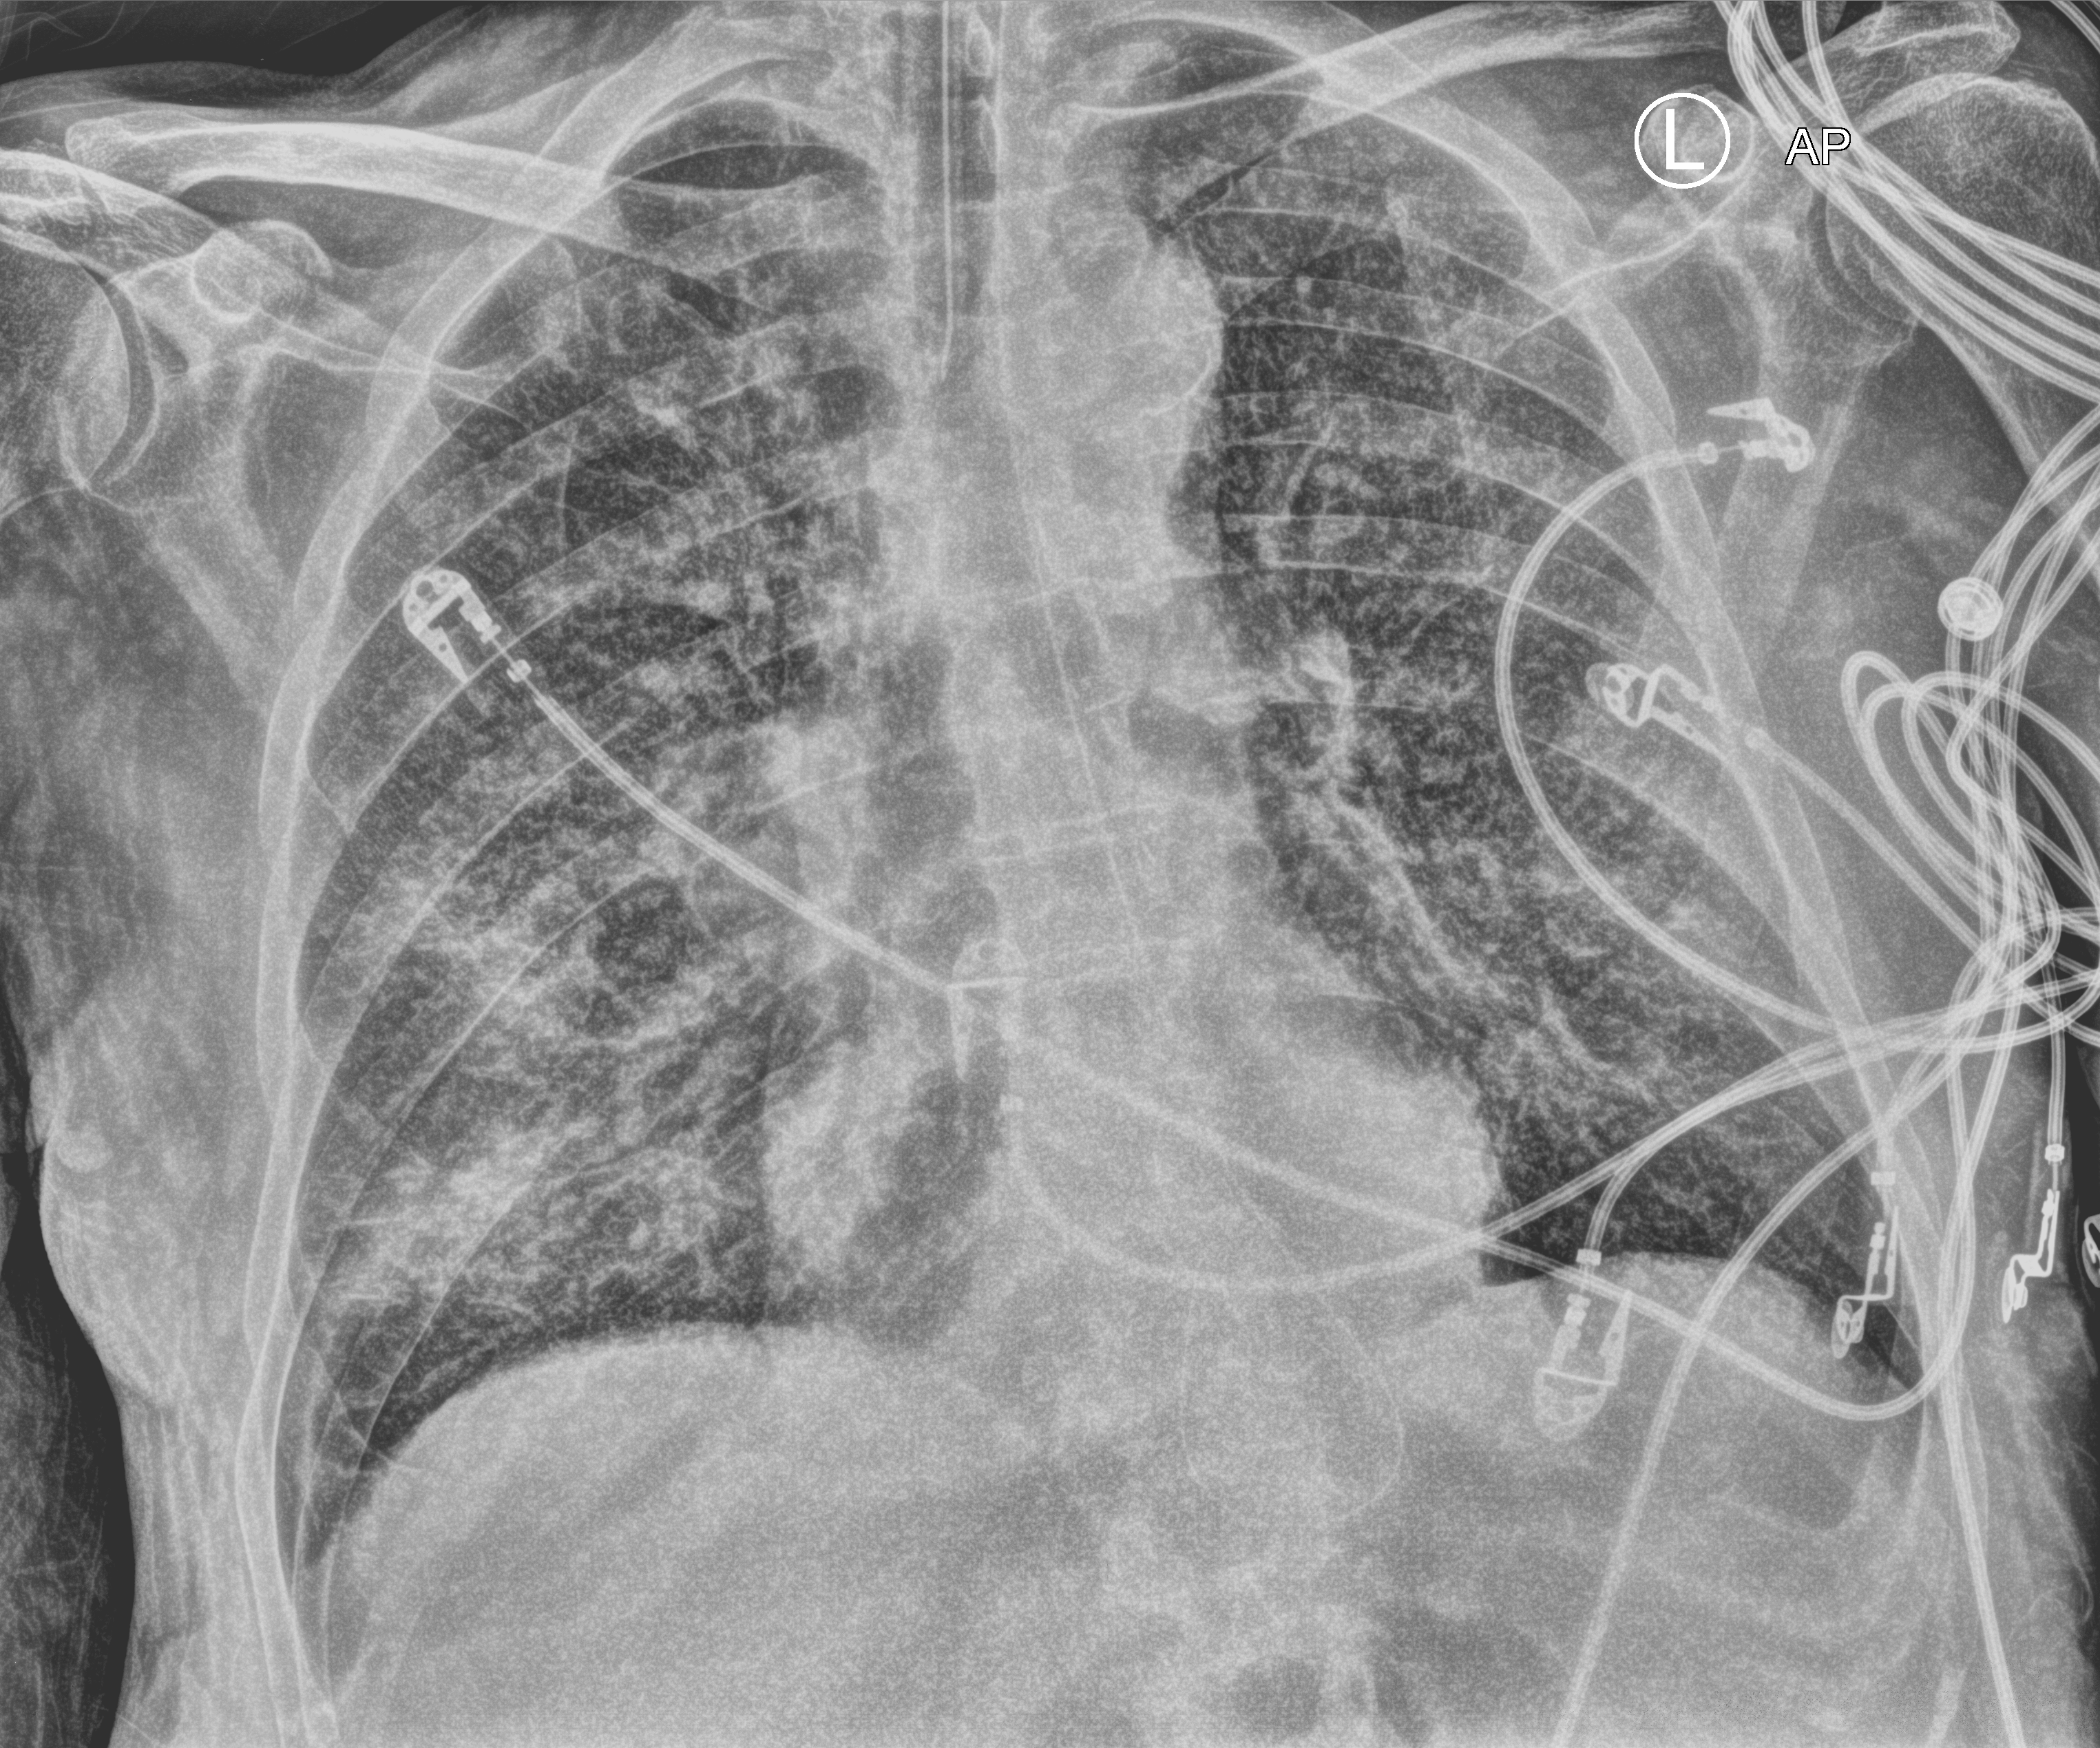
Chest X-ray (portable), anteroposterior (AP) projection. Male patient hospitalised with COVID-19, age 75–90 years.
From the hospital-stay record, not from the radiograph (when in the stay this image was taken is not recorded):
- chronic kidney disease (admission record): no
- admitted to intensive care during this hospital stay: yes